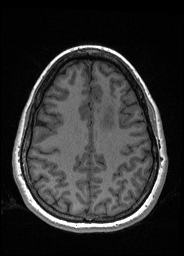
Pre-operative brain MRI before brain-tumour surgery, one axial slice. Position 64 of 176 along the scan axis. T1-weighted post-contrast. 184 × 256 image matrix, field of view 180 × 250 mm. From the clinical record (not read from this slice): histopathology: Oligodendroglioma; WHO grade: 2; IDH mutation: yes.
Structures marked on this image (manually delineated by an expert):
- tumour: box from (x=100, y=100) to (x=116, y=129) px